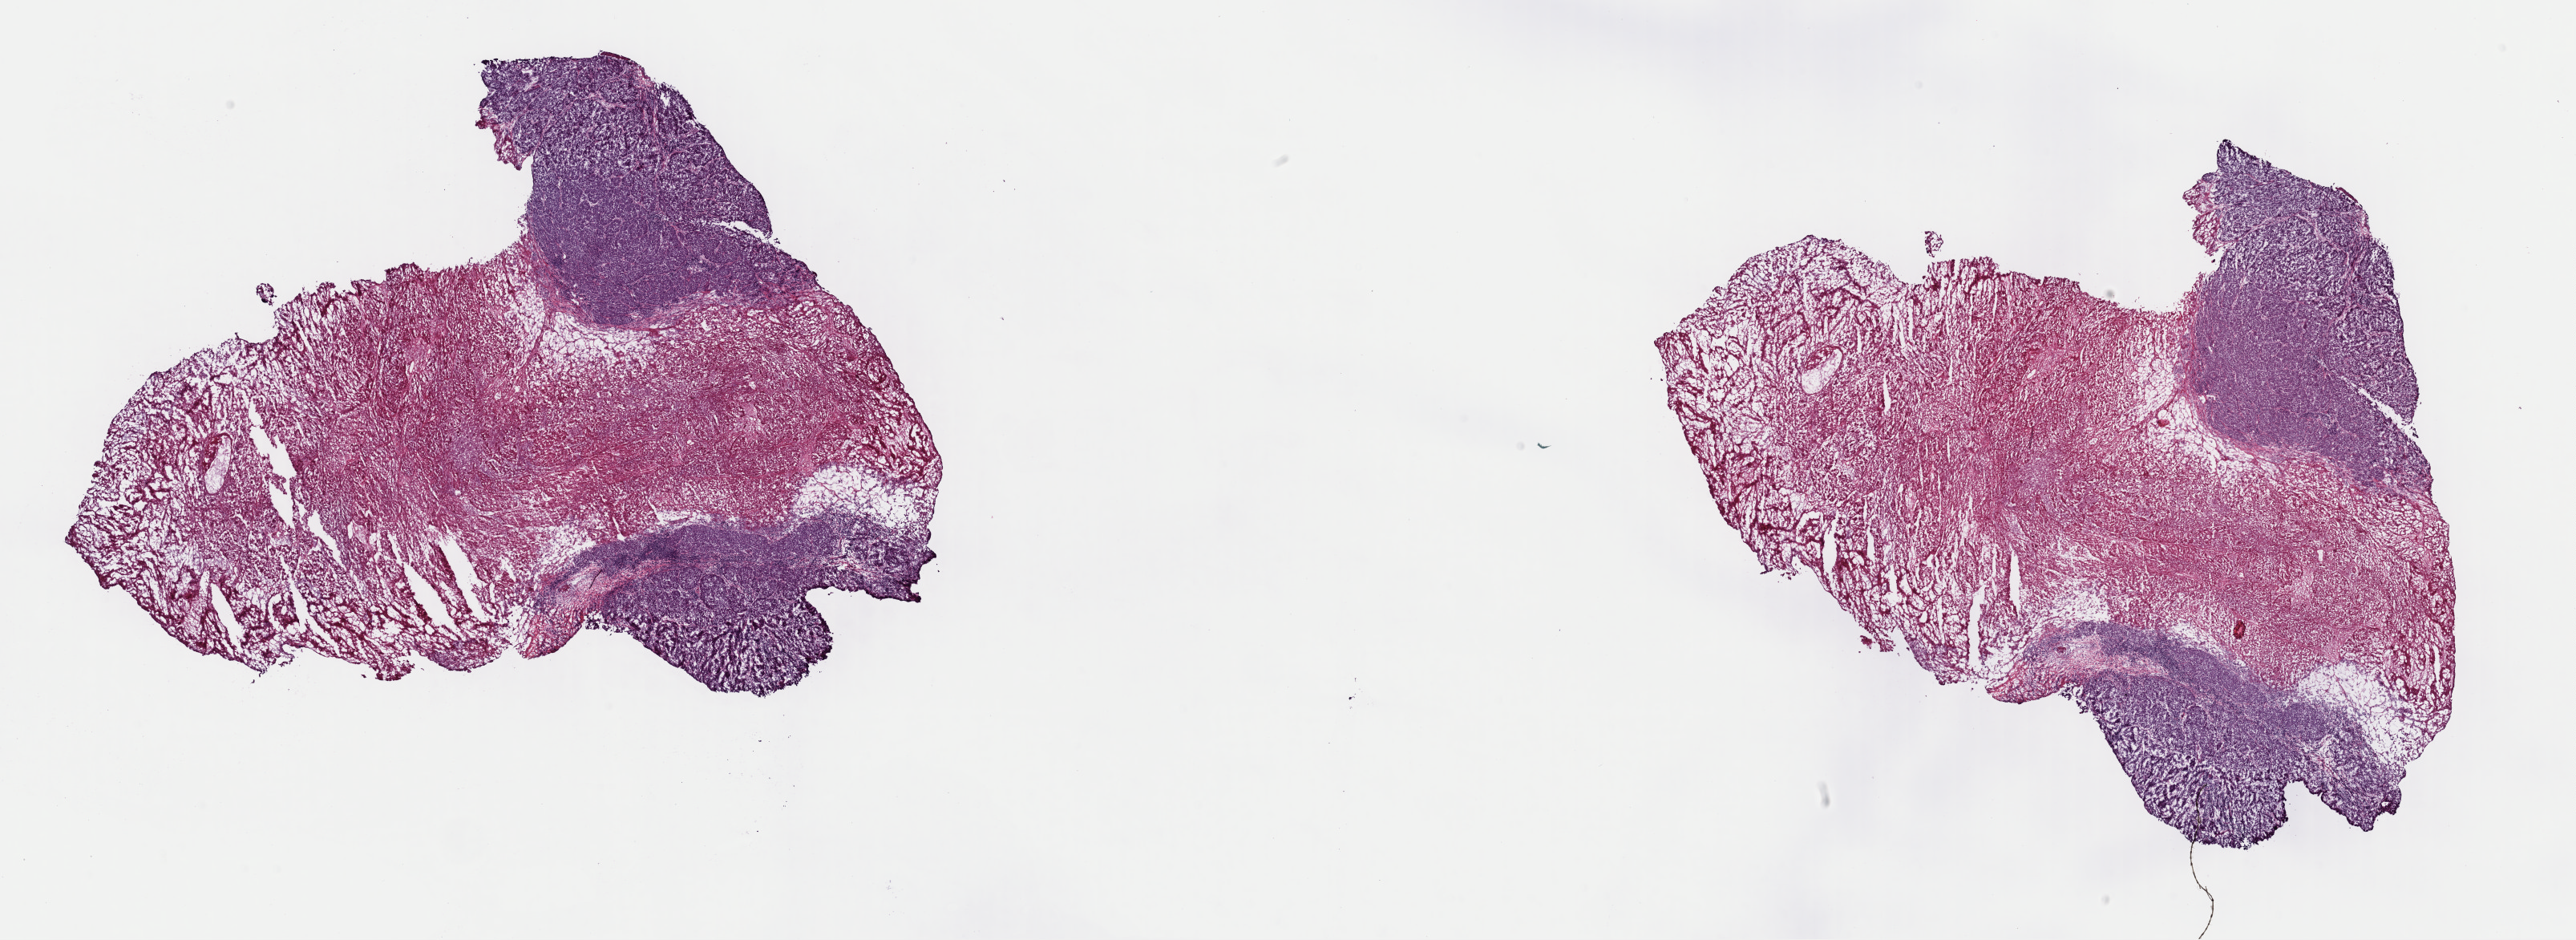
Digitized H&E tissue section (whole slide) — whole scanned area (about 25.4 x 9.3 mm) shown as a low-resolution overview; frozen section from the top of the tissue portion; sample: primary tumour, skin. Patient: male, age at initial diagnosis 69 years. Slide review estimates, as recorded: tumour cells 30%, tumour nuclei 90%, normal cells 0%, stromal cells 65%, necrosis 5%. Infiltration values recorded for this section: lymphocyte infiltration 0%, monocyte infiltration 0%, neutrophil infiltration 0%.
TNM: T4b N0 M0. Histologic diagnosis: Nodular melanoma. AJCC pathologic stage: IIC.